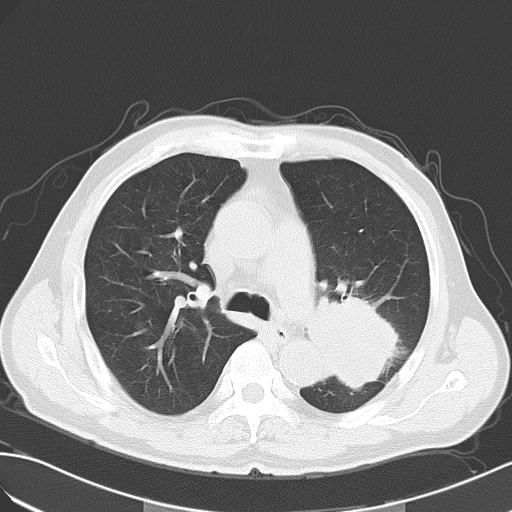
Chest CT, one axial slice; position 36 of 55 along the scan axis; reconstruction kernel B70f; lung window (W 1500 / L -600 HU); 5 mm slice thickness; 512 × 512 image matrix, field of view 353 × 353 mm. Male patient, age 63 years. Case-level facts recorded for this patient, not image findings: clinical TNM (as recorded): T3 N3 M1a.
Annotated regions visible in this slice (rectangle marked by the reading radiologist):
- lung tumour (recorded histology: large cell carcinoma): box from (x=309, y=280) to (x=399, y=398) px